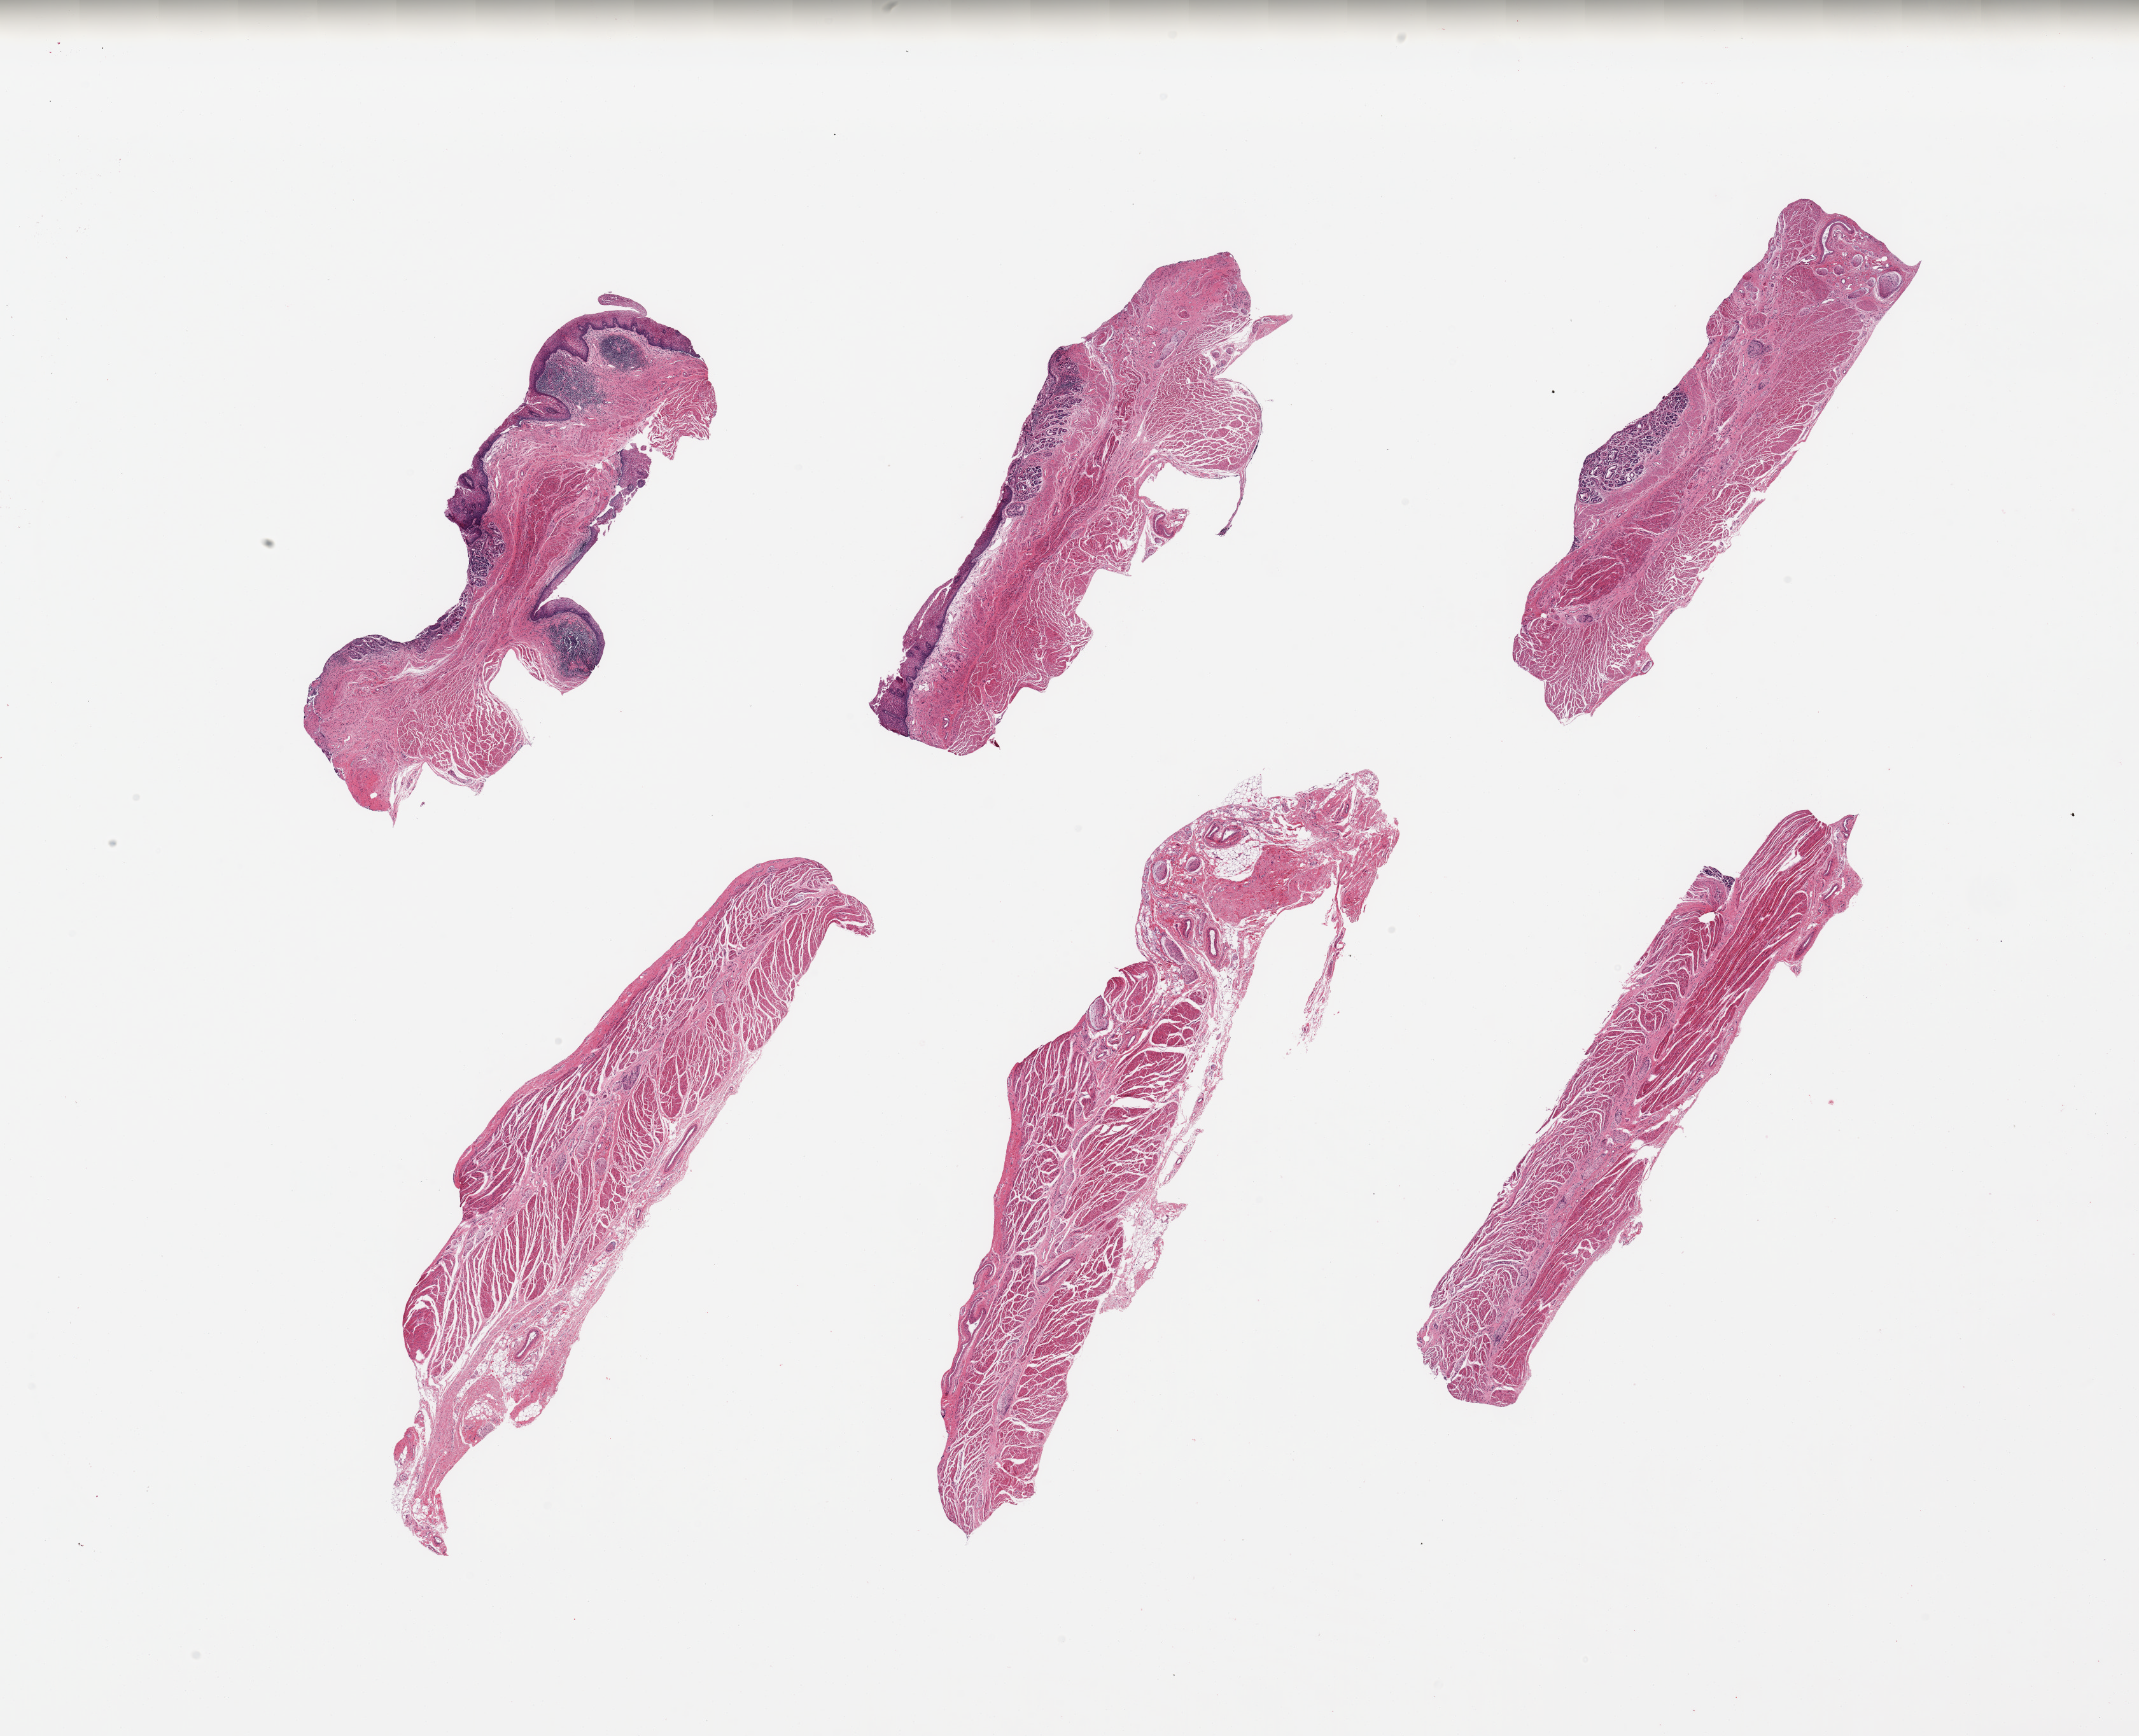
Whole-slide image, hematoxylin and eosin (H&E) stain, shown as a low-resolution overview of the whole scanned area (about 26.6 x 21.6 mm); PAXgene-fixed paraffin-embedded (PFPE) section; sampled site (target tissue): gastroesophageal junction; donor tissue sample. Female donor.
Reviewer comment on this tissue sample: 6 pieces; 3 pieces with mildly to moderately autolyzed gastric and esophageal mucosa and lymphoid aggregates, not target tissue; target muscularis well preserved.